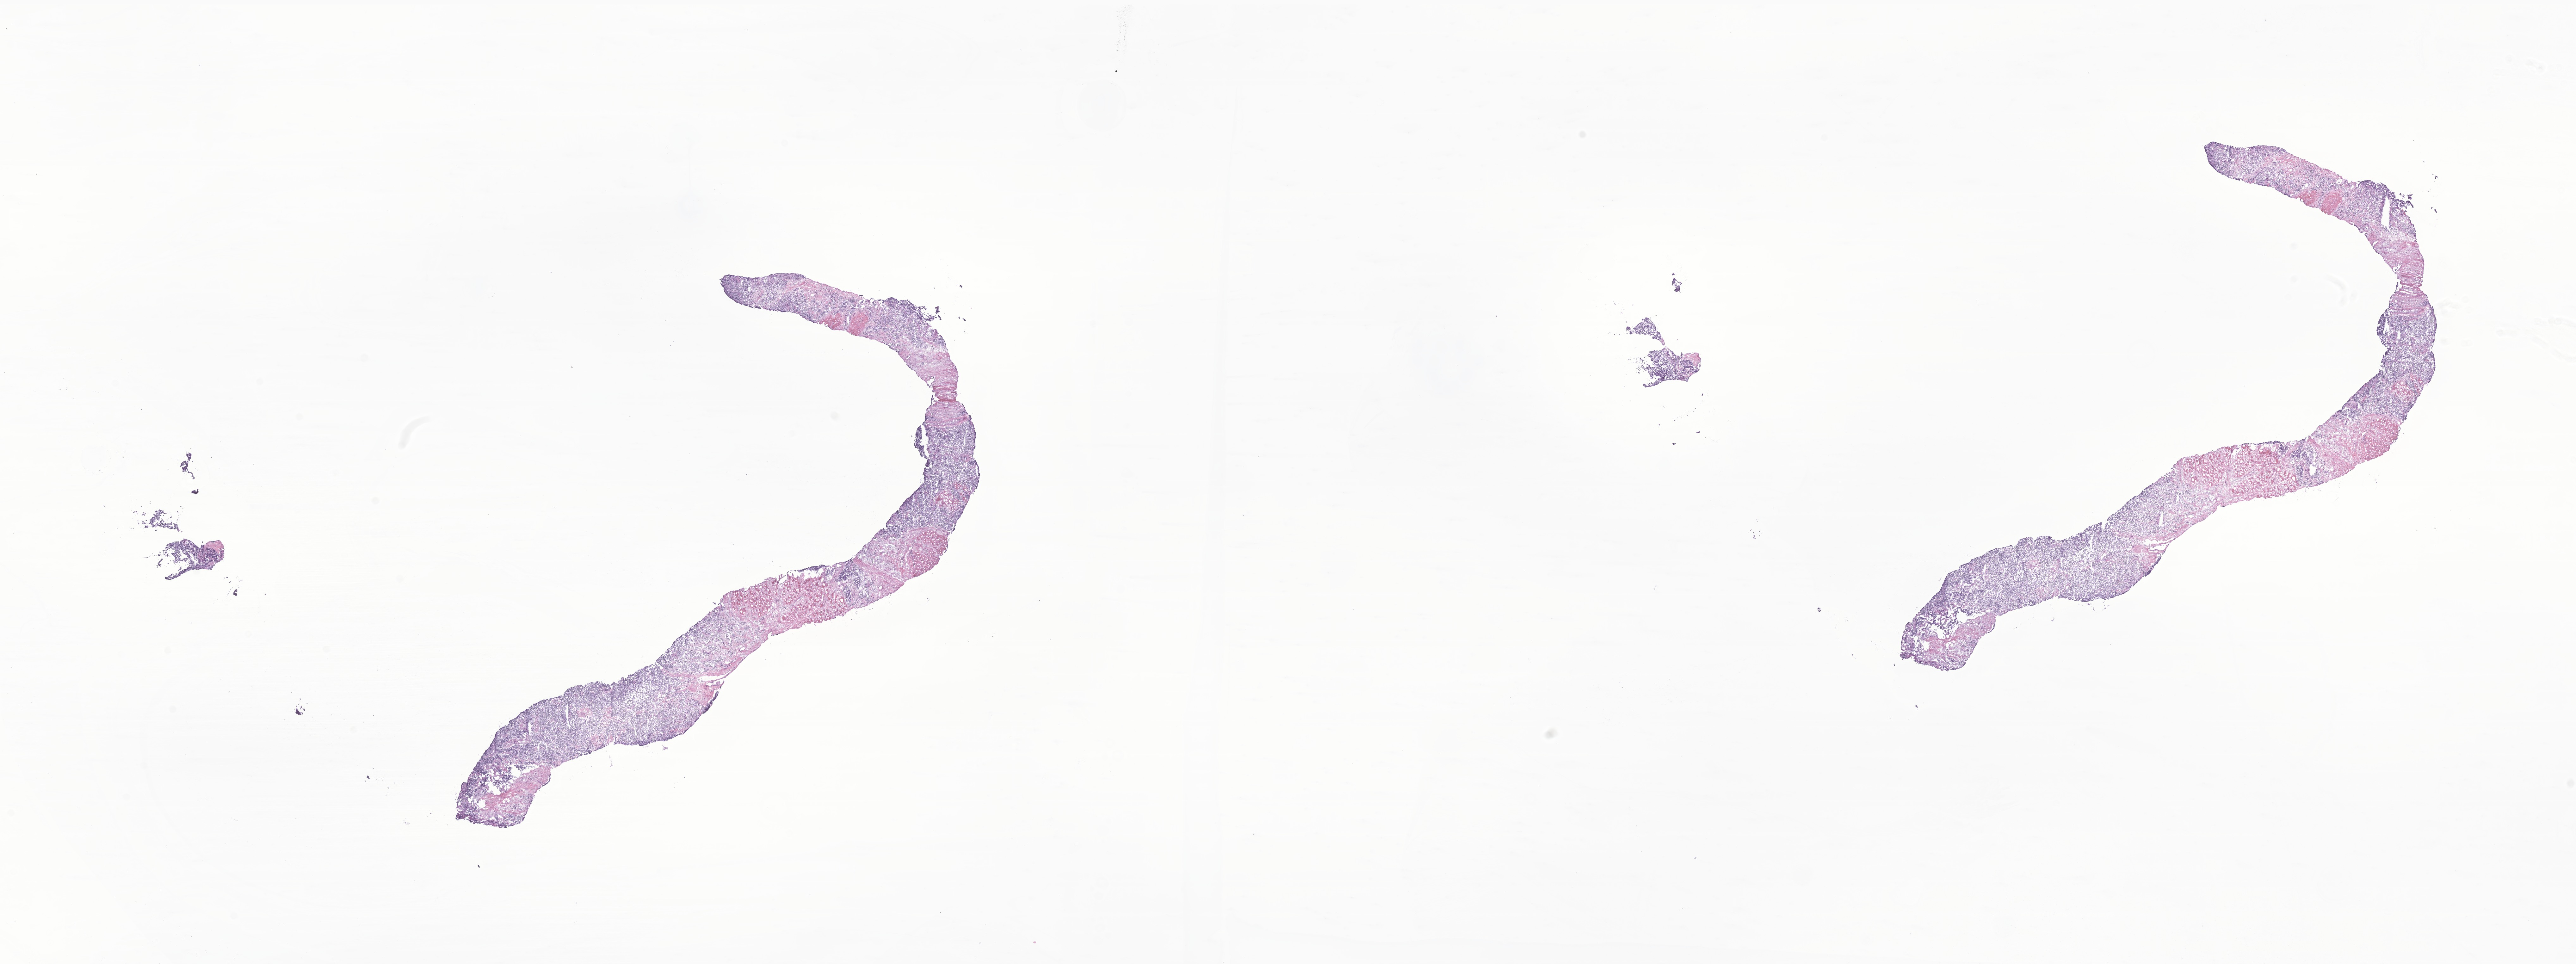
Whole-slide image, hematoxylin and eosin (H&E) stain of tumor tissue from the peritoneum — a low-resolution overview of the entire scanned area, about 34.3 x 12.9 mm. Frozen section (OCT-embedded). Patient male; age 174 months (14 years 6 months).
* diagnosis (ICD-O-3 morphology term): Alveolar rhabdomyosarcoma